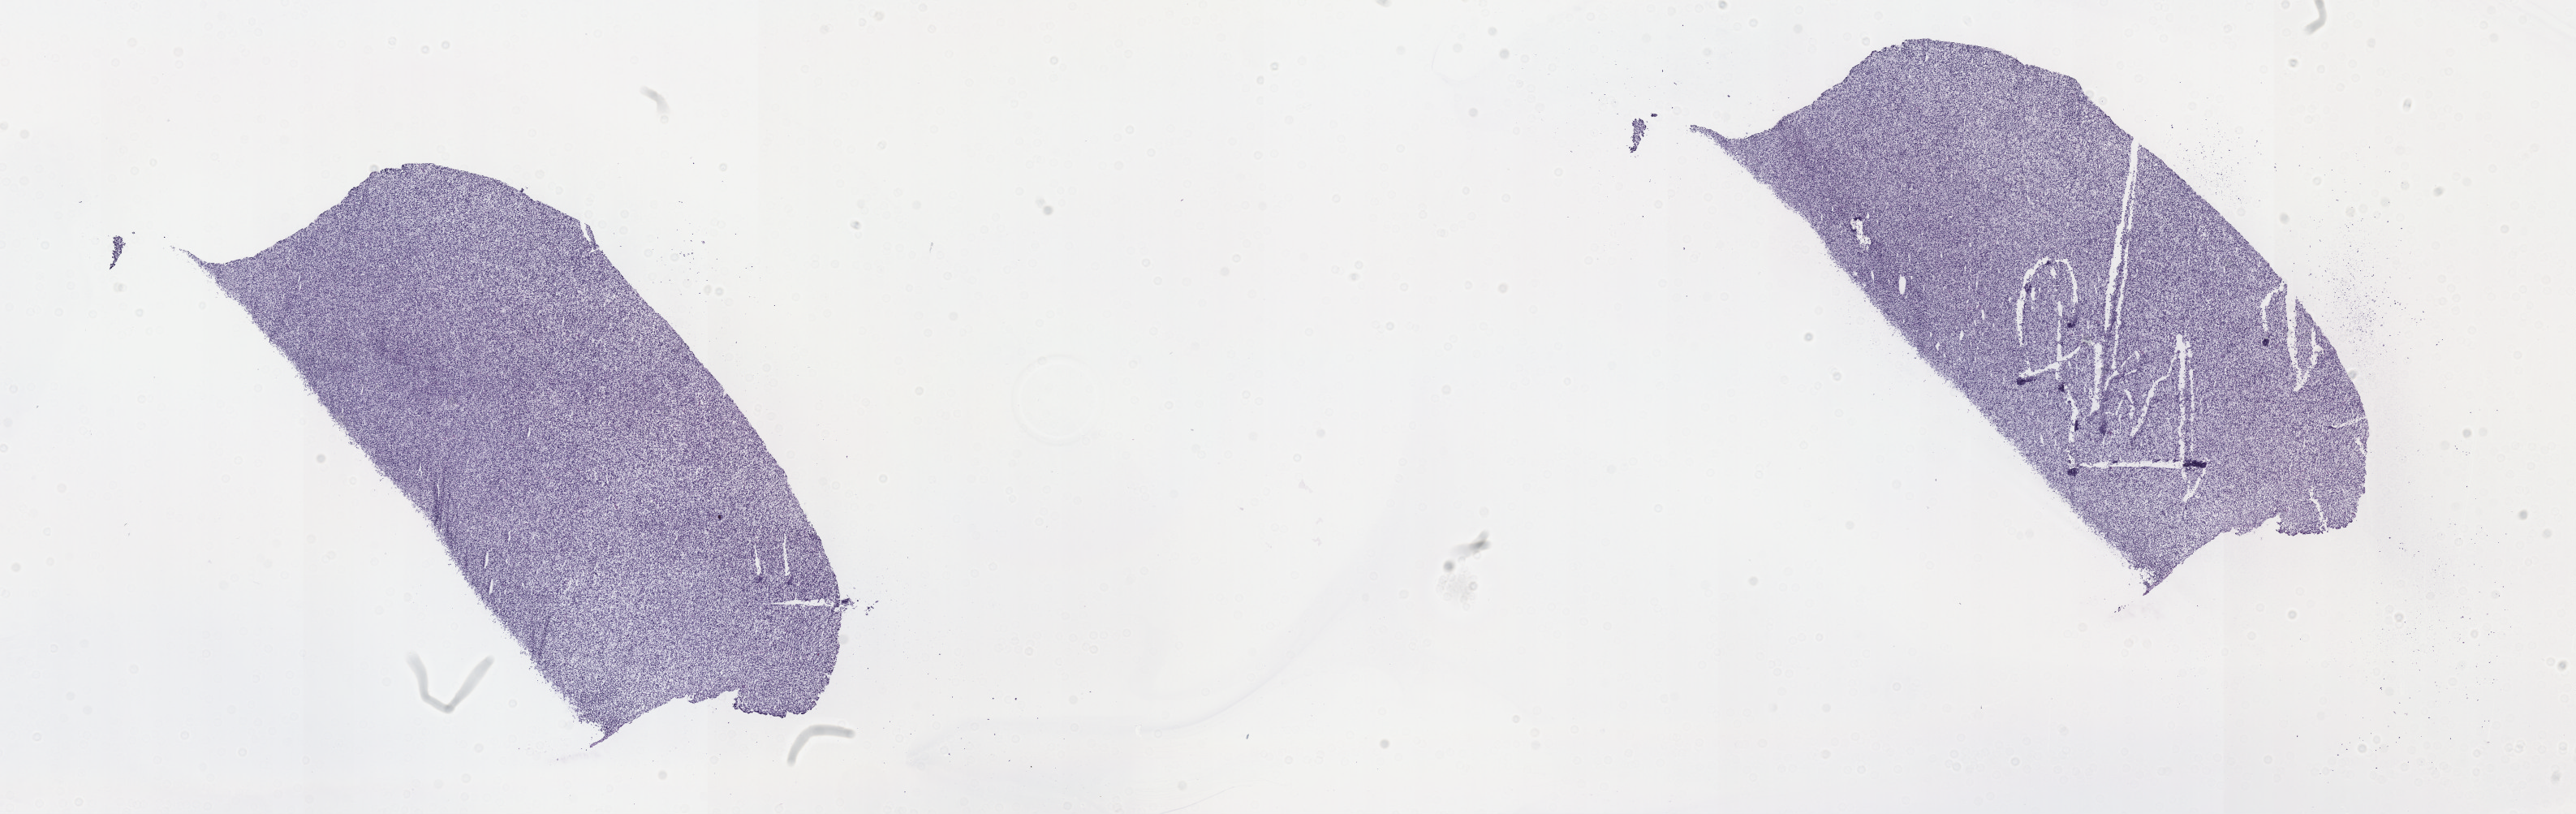
Whole-slide histology image, H&E, shown as a low-resolution overview of the whole scanned area (about 25.7 x 8.1 mm, acquisition: 40x scan); frozen section; retroperitoneum and peritoneum, primary tumour sample. Patient: male, age at initial diagnosis 57 years. Slide review estimates, as recorded: tumour cells 100%, tumour nuclei 95%, normal cells 0%, stromal cells 0%, necrosis 0%. Infiltration values recorded for this section: lymphocyte infiltration 0%, monocyte infiltration 0%, neutrophil infiltration 0%.
Histologic diagnosis: Dedifferentiated liposarcoma (retroperitoneum).